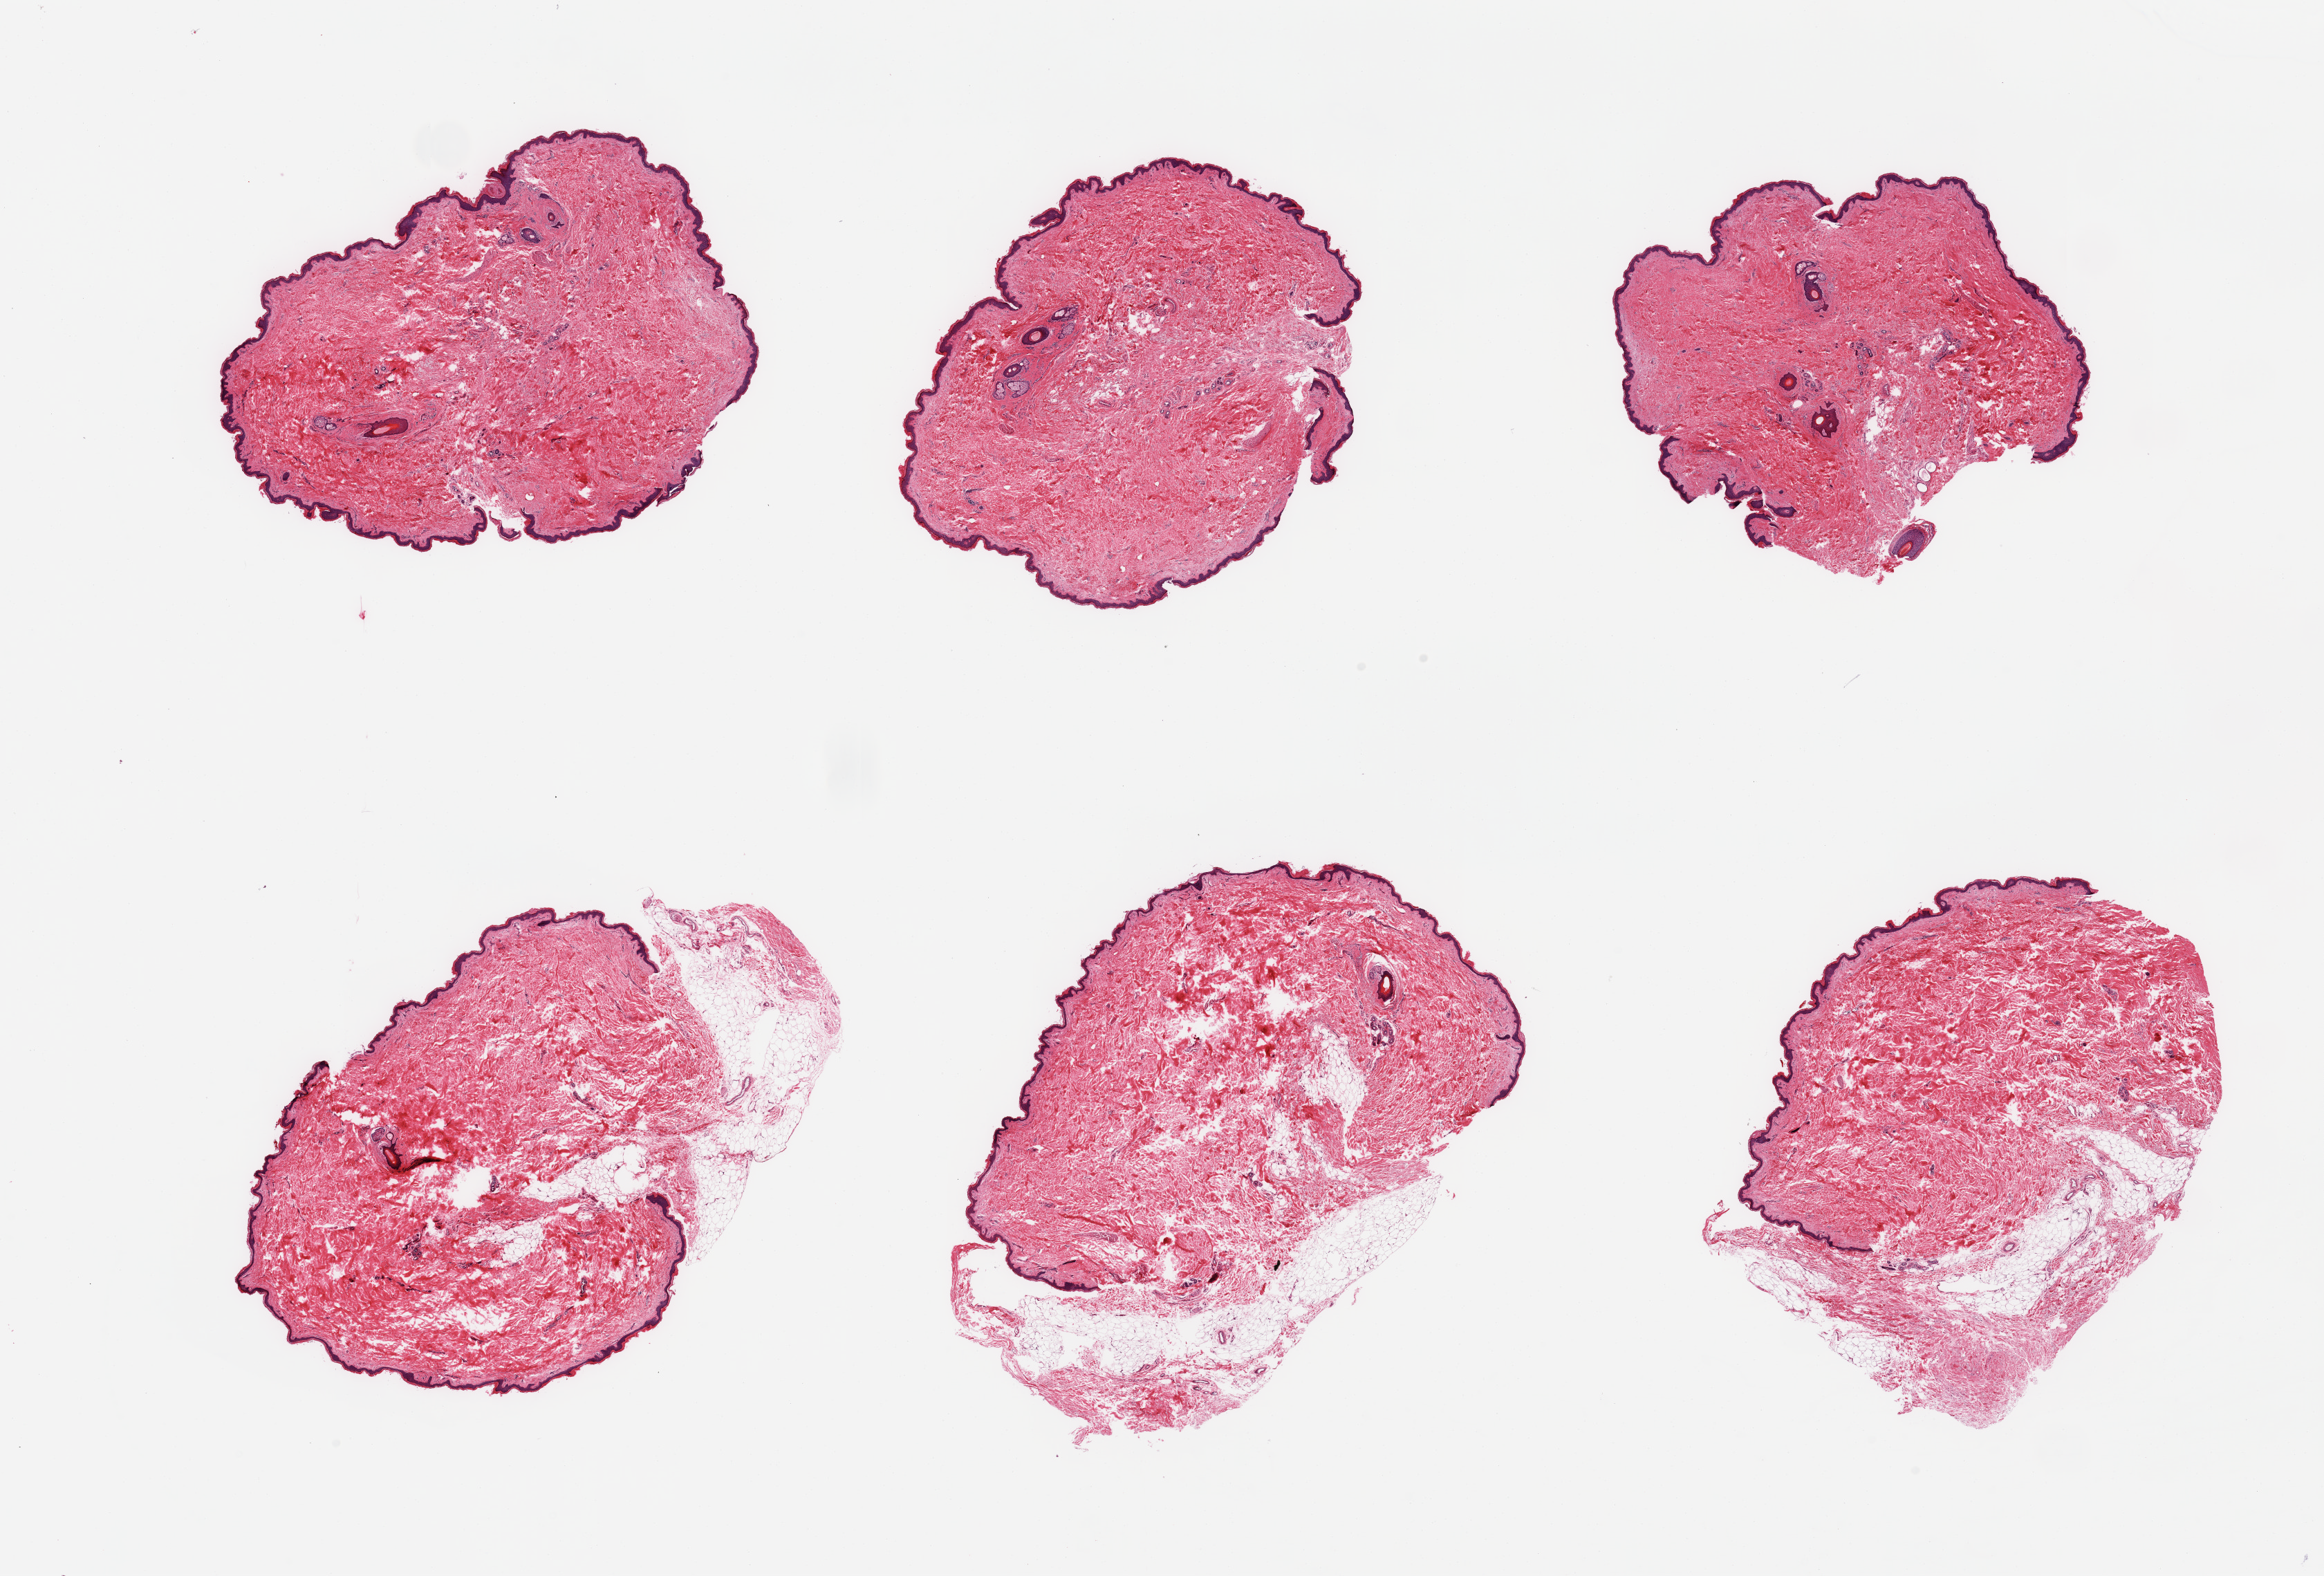
Hematoxylin and eosin (H&E) whole-slide image, low-resolution overview of the scanned area, about 26.6 x 18.0 mm (slide scanned at 20x). PAXgene-fixed paraffin-embedded (PFPE) section. Section of skin of suprapubic region (target tissue). Tissue donor sample. Donor sex: female.
- review note (as recorded): 6 pieces; 3 are well trimmed, 3 include ~5-10 % attached fat